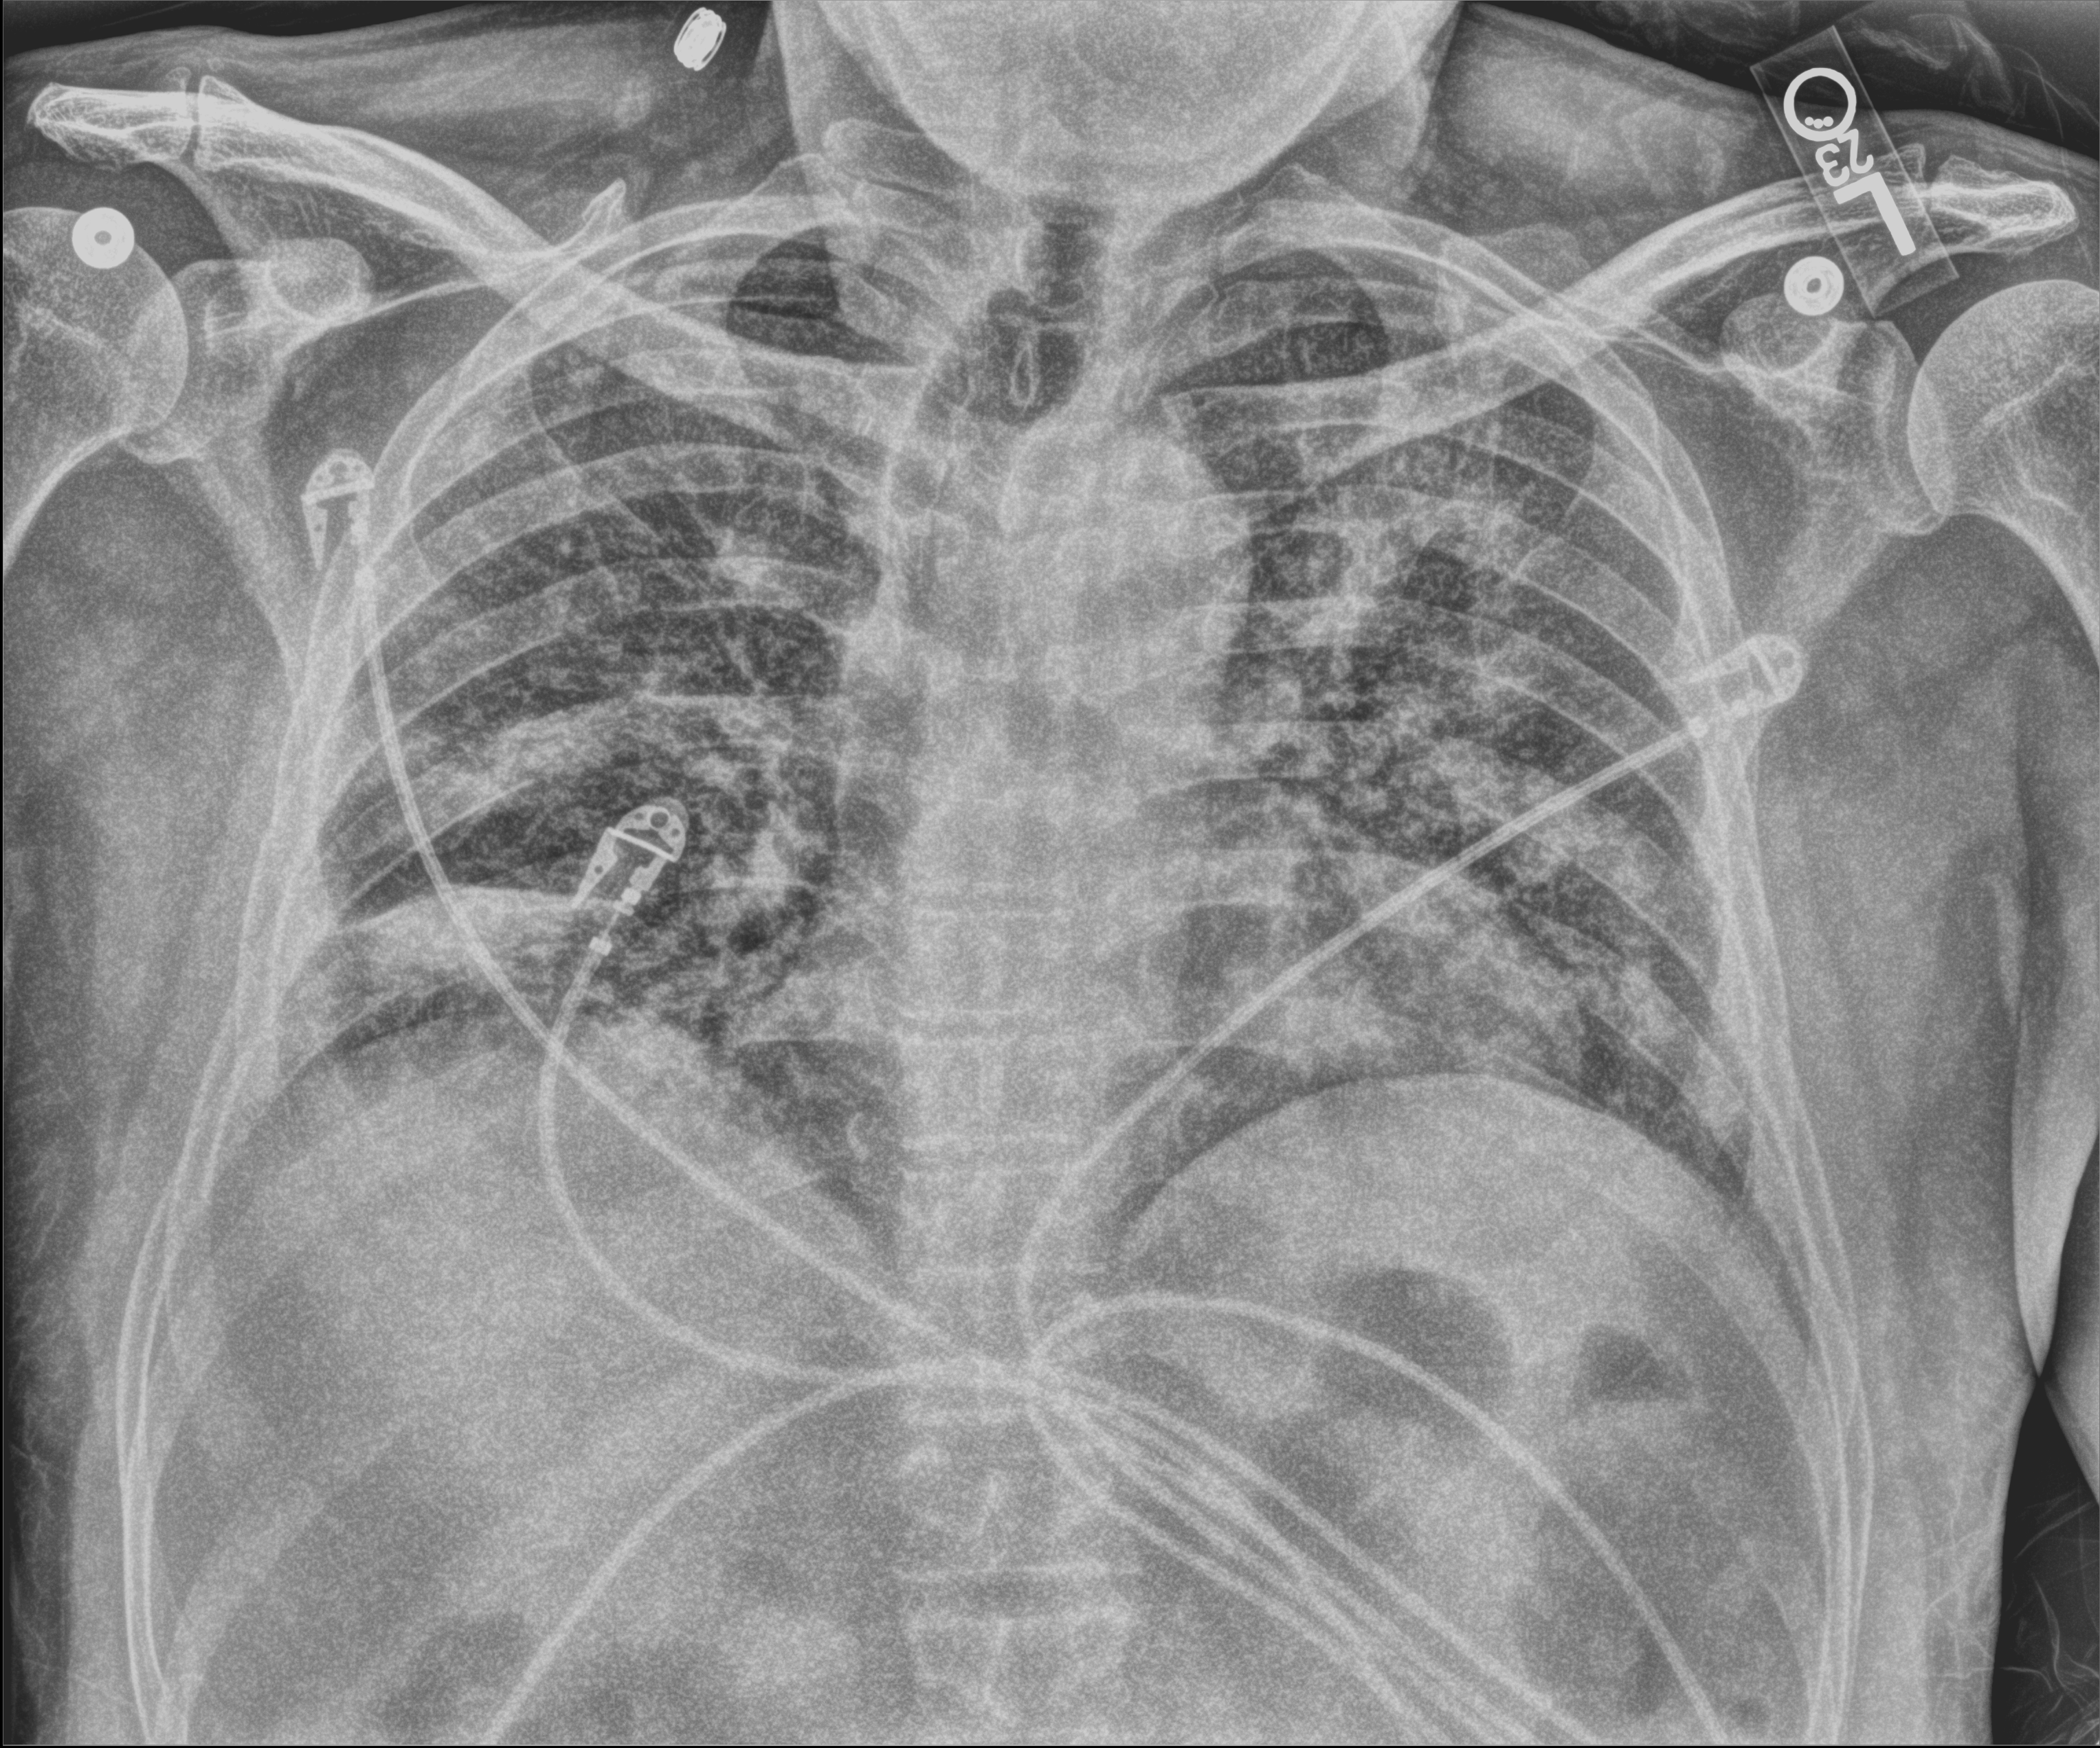
Bedside chest radiograph (computed radiography); anteroposterior (AP) projection. Male patient hospitalised with COVID-19, age 18–59 years.
Admission-level facts for this patient (not findings on this image; timing relative to this image not recorded):
- COPD (admission record): no
- admitted to intensive care during this hospital stay: no